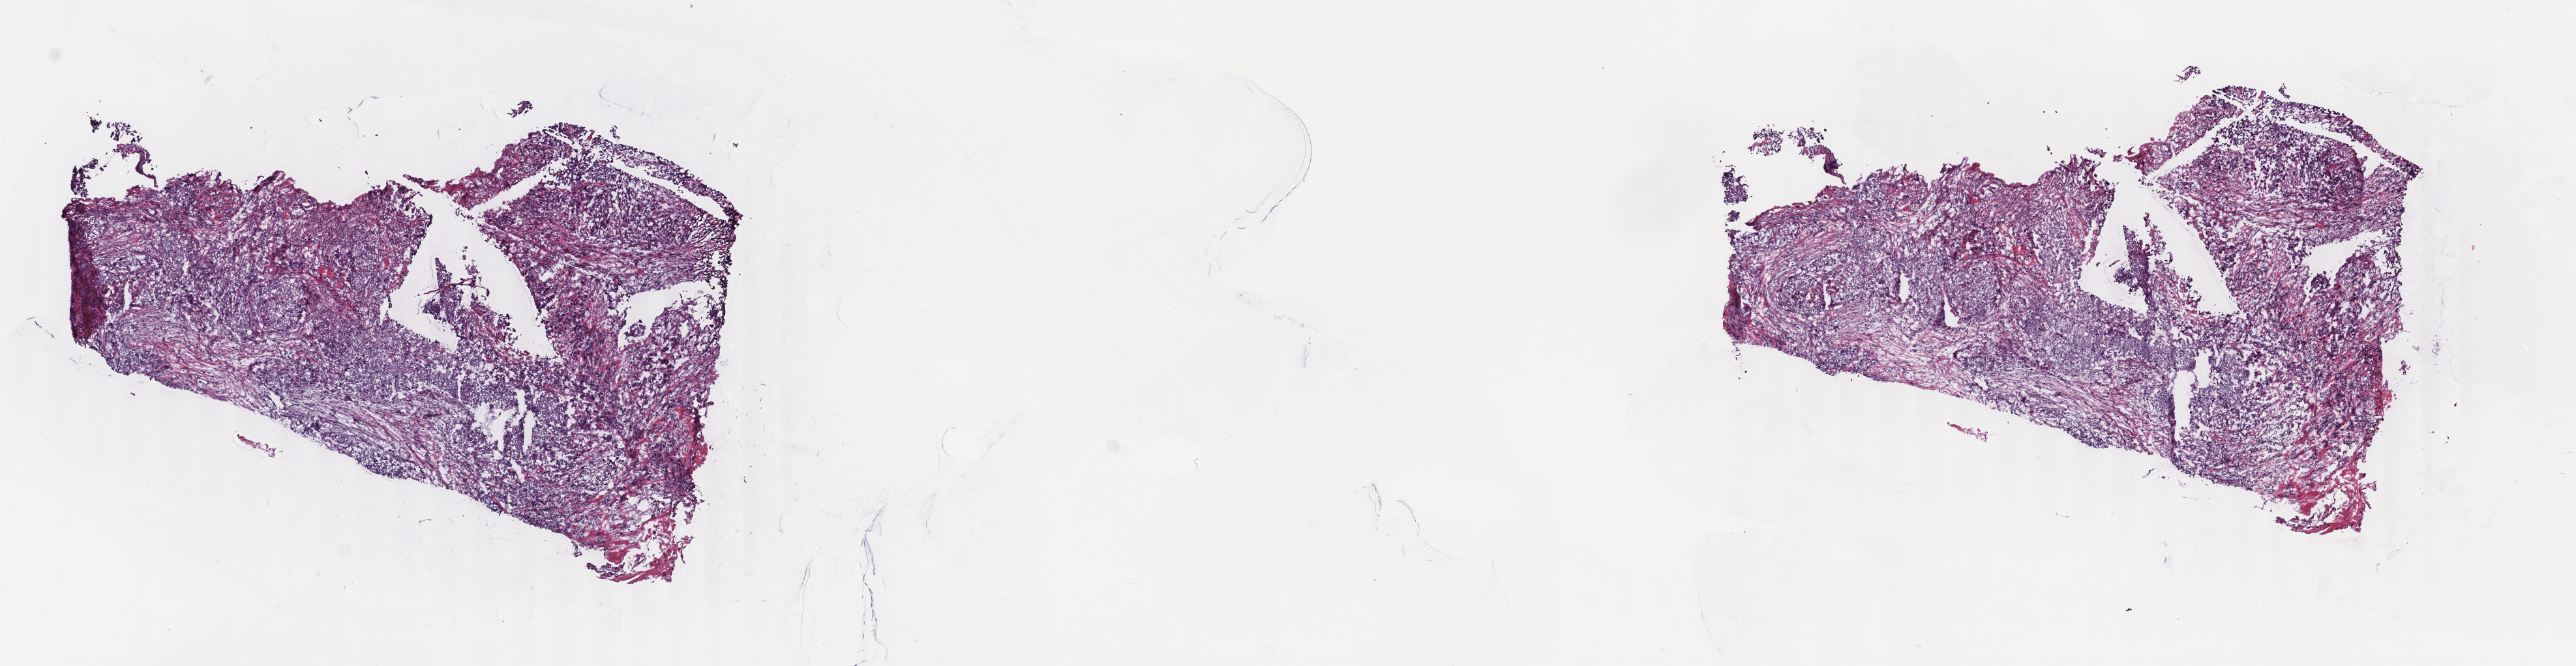
Hematoxylin and eosin (H&E) stained whole-slide image, a low-resolution overview of the entire scanned area, about 15.7 x 4.1 mm. Frozen section from the top of the tissue portion. Sample: primary tumour, breast. Patient: female, age at initial diagnosis 85 years. Slide review estimates, as recorded: tumour cells 70%, tumour nuclei 70%, normal cells 0%, stromal cells 20%, necrosis 10%. Inflammatory infiltration, as recorded: lymphocyte infiltration 0%, monocyte infiltration 0%, neutrophil infiltration 0%.
• histologic diagnosis: Infiltrating duct carcinoma, NOS
• AJCC pathologic stage: IIB
• laterality: right